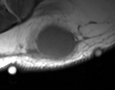
MRI of an extremity soft-tissue mass, one axial slice; MR volume resampled by the dataset authors to the PET/CT grid (not the native acquisition matrix); 115 × 90 image matrix, field of view 112 × 88 mm. Male patient. From the clinical record (not read from this slice): histological type: pleiomorphic leiomyosarcoma; grade: high; site of the primary tumour: left buttock.
Outlined on this slice (expert contour drawn on MRI and transferred to this co-registered scan by the dataset authors):
- gross tumour volume including surrounding oedema: bounding box [x1, y1, x2, y2] px = [28, 23, 77, 61]
- gross tumour volume (mass): [28, 25, 77, 60]